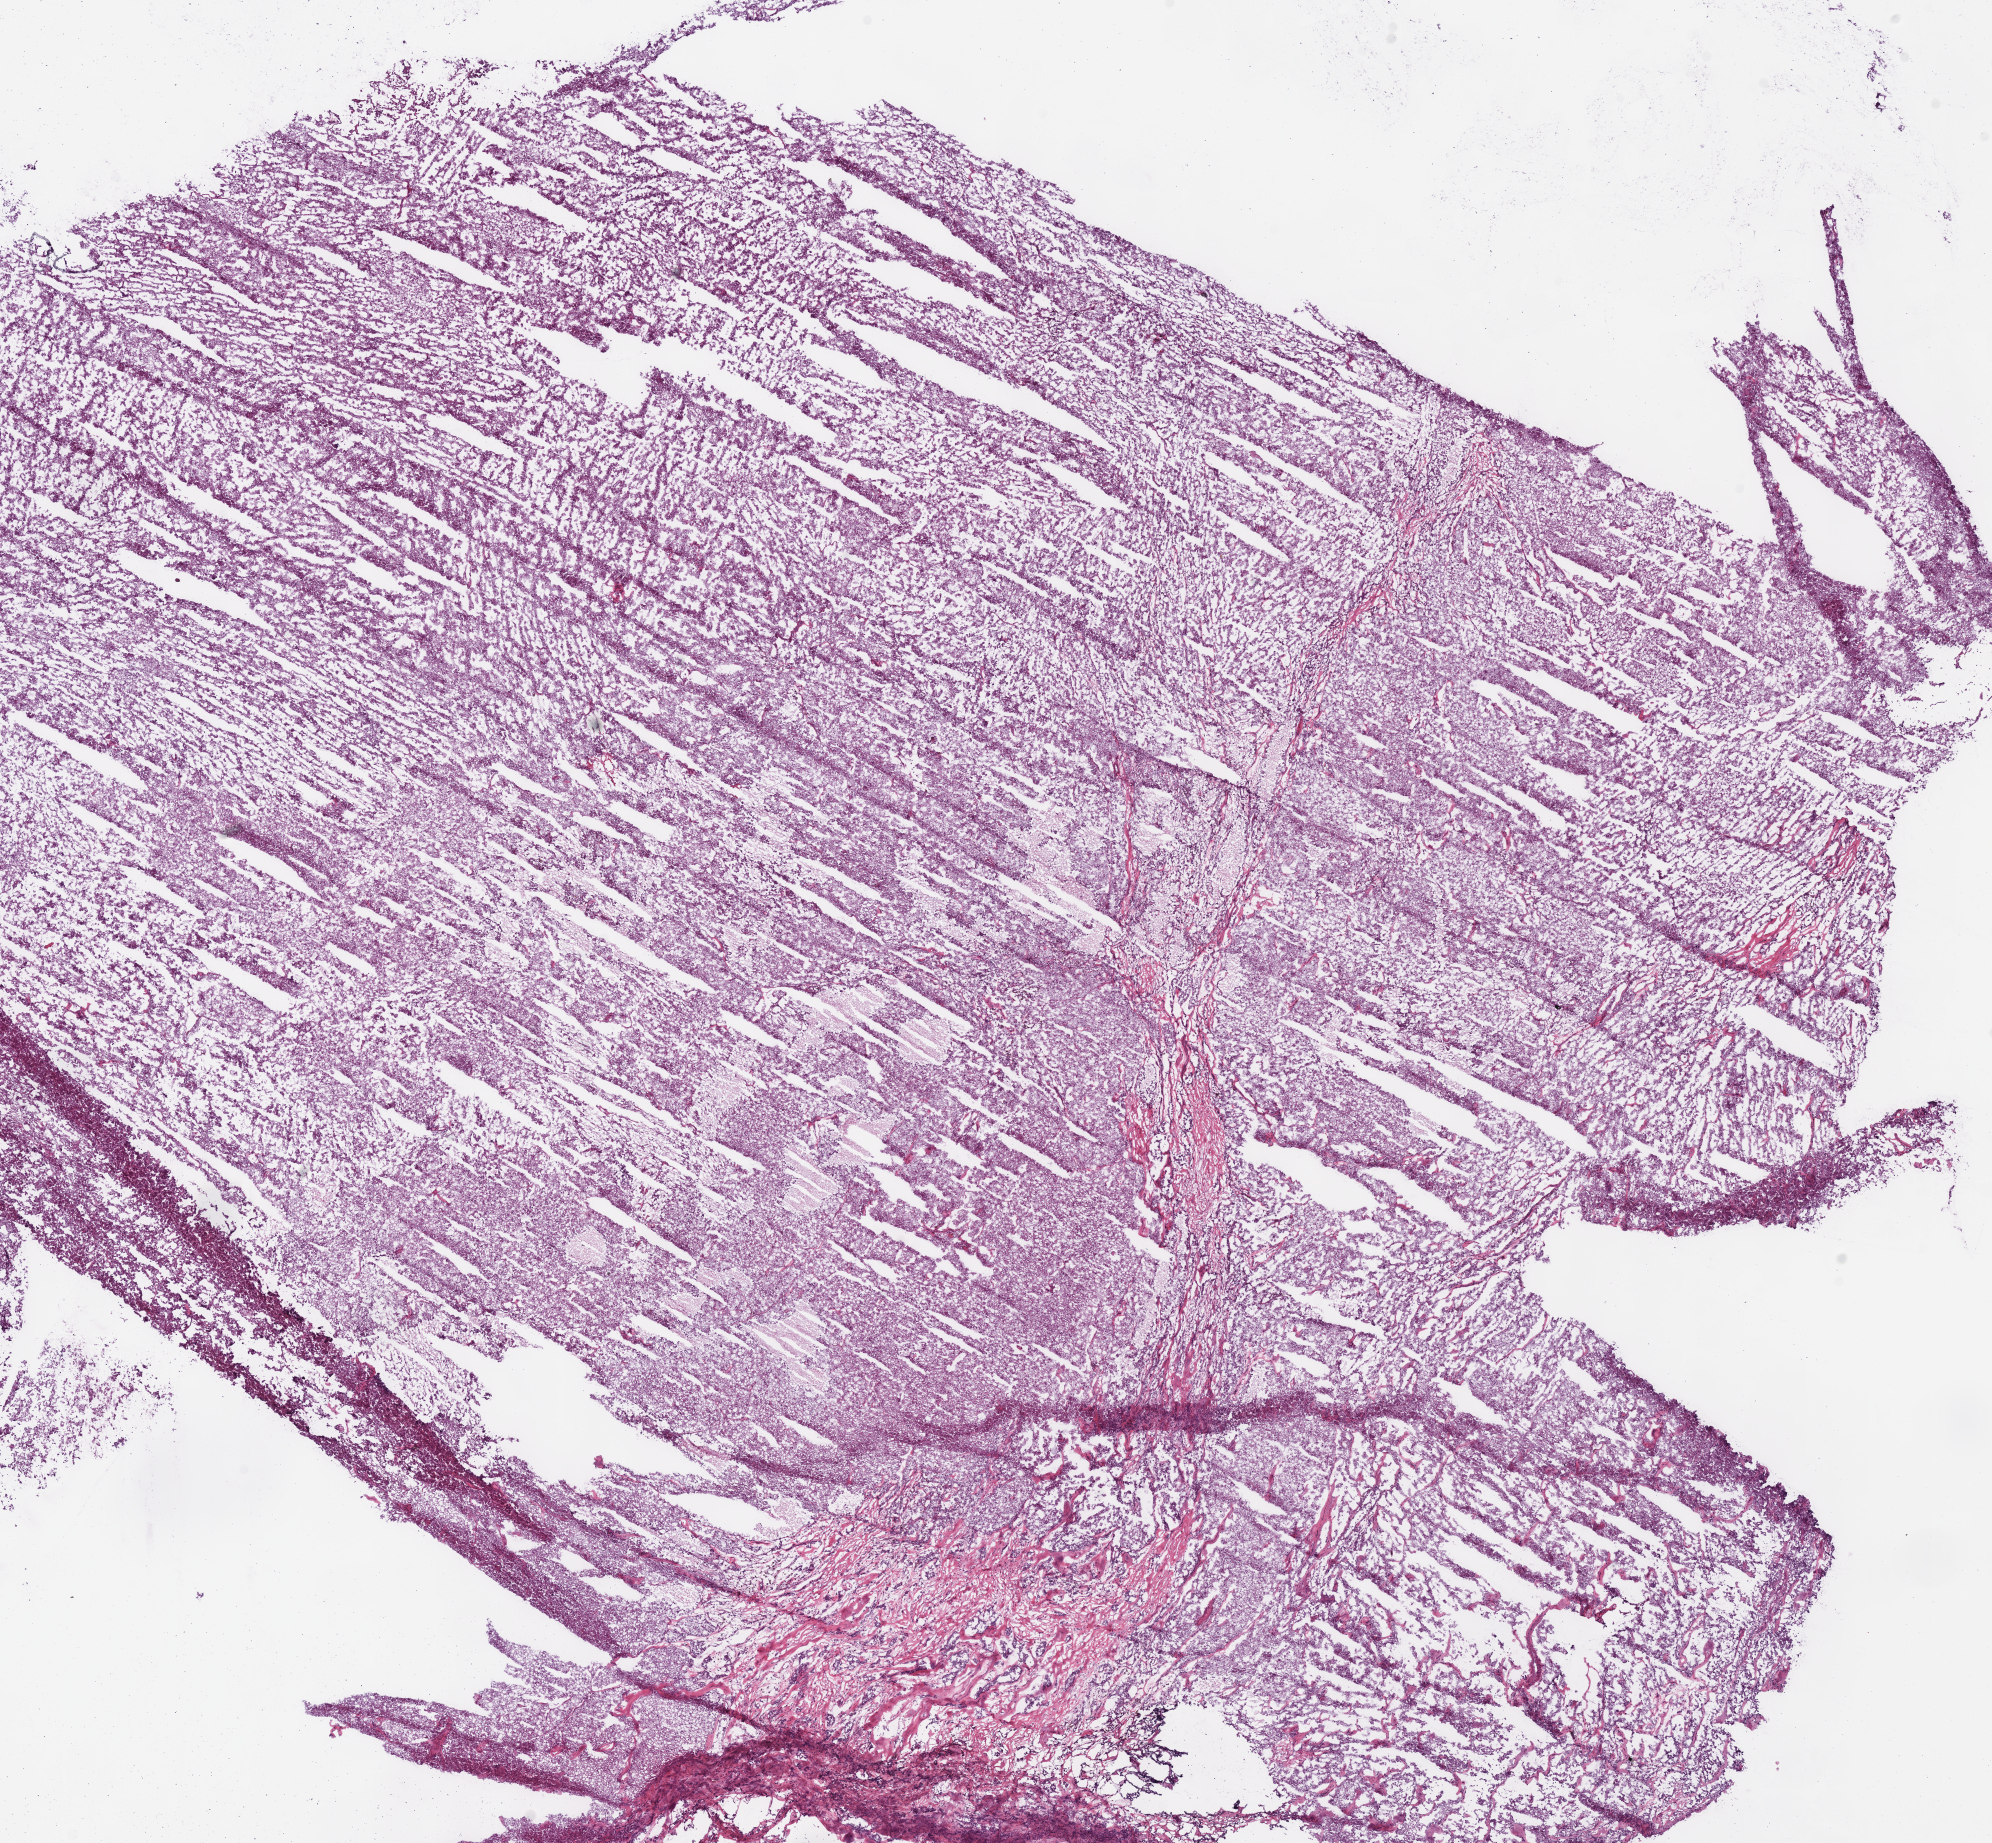
Digitized Hematoxylin and eosin (H&E) stained tissue section (whole slide), low-resolution overview of the scanned area, about 15.7 x 14.5 mm (slide scanned at 40x), frozen section from the bottom of the tissue portion, sample: primary tumour, kidney. Female, age 57 years at initial diagnosis. Pathologist review of this section (percent, as recorded): tumour cells 93%, tumour nuclei 85%, normal cells 0%, stromal cells 7%, necrosis 0%. Inflammatory infiltration, as recorded: lymphocyte infiltration 5%, monocyte infiltration 0%, neutrophil infiltration 0%.
- diagnosis: Renal cell carcinoma, chromophobe type
- lymph nodes positive (case pathology): 0 of 1 examined
- AJCC pathologic stage: I (6th edition)